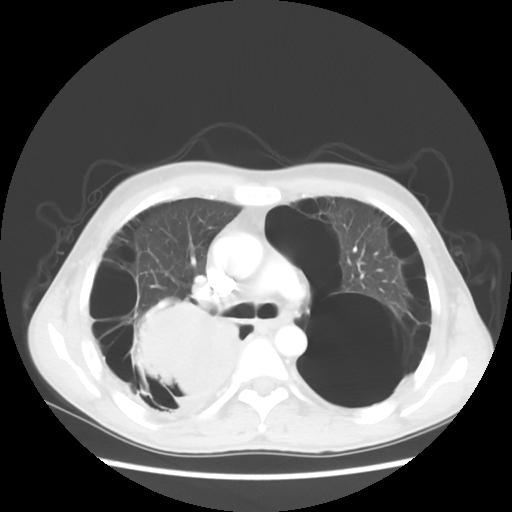
Chest CT, one axial slice. Slice 35 of 56 in the series (ordered by position). 140 kVp. Lung window (W 1500 / L -600 HU). 5 mm slice thickness. 512 × 512 image matrix, field of view 351 × 351 mm. Patient: male, 41 years. From the clinical record (not read from this slice): clinical TNM (as recorded): T4 N0 M1a.
Structures marked on this image (bounding box drawn by a radiologist):
- lung tumour (recorded histology: large cell carcinoma): bounding box <132,300,250,412> (left, top, right, bottom; pixels)